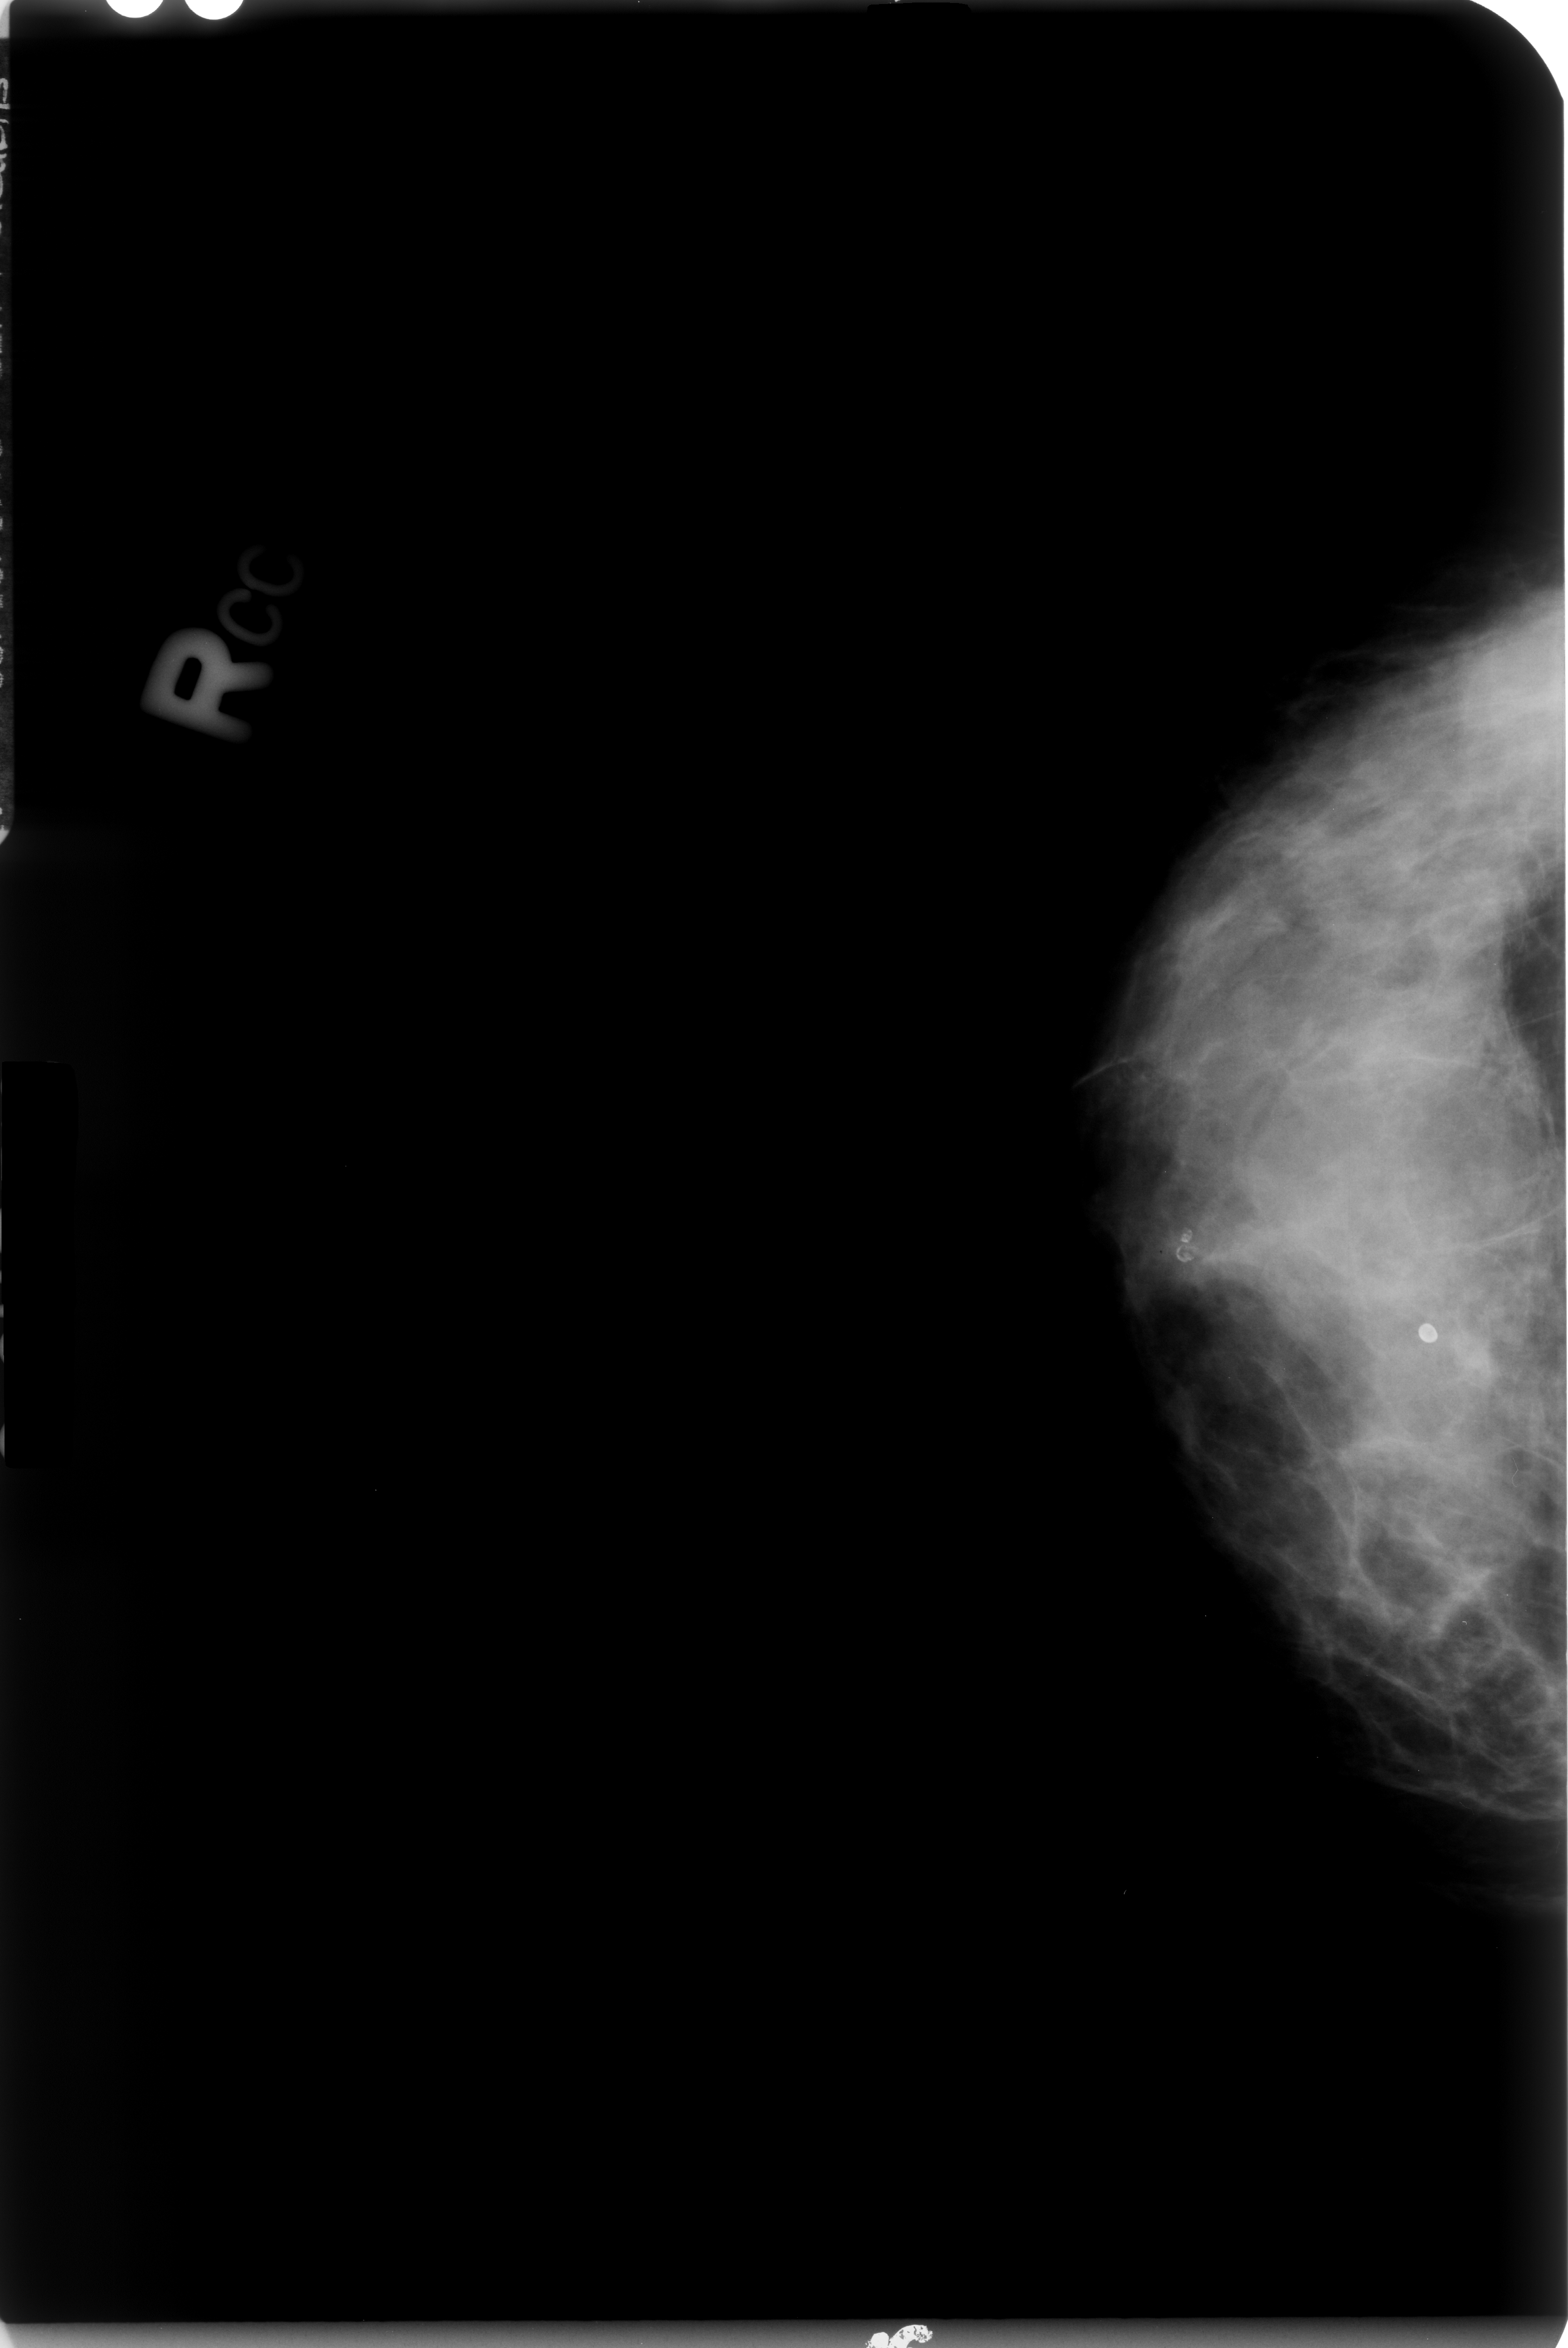
Scanned film-screen mammogram; right breast; craniocaudal (CC) view; BI-RADS breast density category 3 (scale 1–4).
Marked findings (only marked abnormalities are described; nothing is implied about the rest of the image): Finding 1 of 2: calcifications, morphology lucent center; BI-RADS assessment category 2; subtlety rating 5 on a 1 (subtle) to 5 (obvious) scale; benign; no additional work-up was recommended (benign without callback). Finding 2 of 2: calcifications, morphology lucent center; BI-RADS assessment category 2; benign without callback (not worked up further).